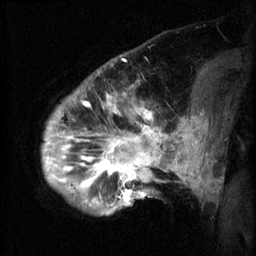
Breast MRI (dynamic contrast-enhanced), one sagittal slice; position 14 of 60 along the scan axis; 3 images stored at this slice position (order not interpretable as contrast timing); 1.5 T; TE 4.2 ms, TR 8.2 ms; 256 × 256 image matrix, field of view 200 × 200 mm. Female patient, age 50 years.
Structures marked on this image (semi-automatic segmentation, software-assisted and operator-edited):
- analysis volume of interest (the breast-tissue region the enhancement analysis was run in; not a lesion): bounding box (x1, y1, x2, y2) in pixels: (50, 64, 169, 217)
- tumour enhancement mask (voxels above the 70 % enhancement threshold inside the analysis volume of interest): (50, 94, 169, 207)